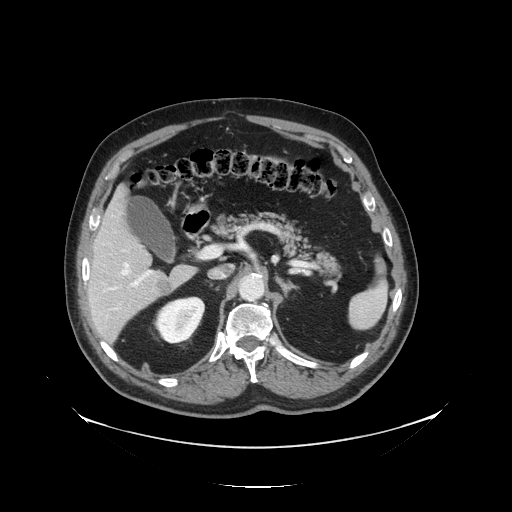
Contrast-enhanced abdominal CT, one axial slice; slice 78 of 138 in the series (ordered by position); reconstruction kernel STANDARD; 120 kVp; soft-tissue window (W 400 / L 40 HU); 2.5 mm slice thickness; 512 × 512 image matrix, field of view 497 × 497 mm. Male patient, age 77 years. Case-level facts recorded for this patient, not image findings: diagnosis: colorectal cancer liver metastases, imaged before liver resection; multiple liver metastases: no; largest metastasis: 1.5 cm.
Annotated regions visible in this slice (manually delineated by an expert):
- hepatic veins: box from (x=121, y=262) to (x=129, y=275) px
- liver: (x=87, y=189)–(x=196, y=343)
- planned liver remnant (the part of the liver to remain after resection): (x=87, y=189)–(x=154, y=287)
- portal vein (with intrahepatic branches): (x=115, y=253)–(x=205, y=310)
- liver metastasis: (x=157, y=280)–(x=173, y=297)